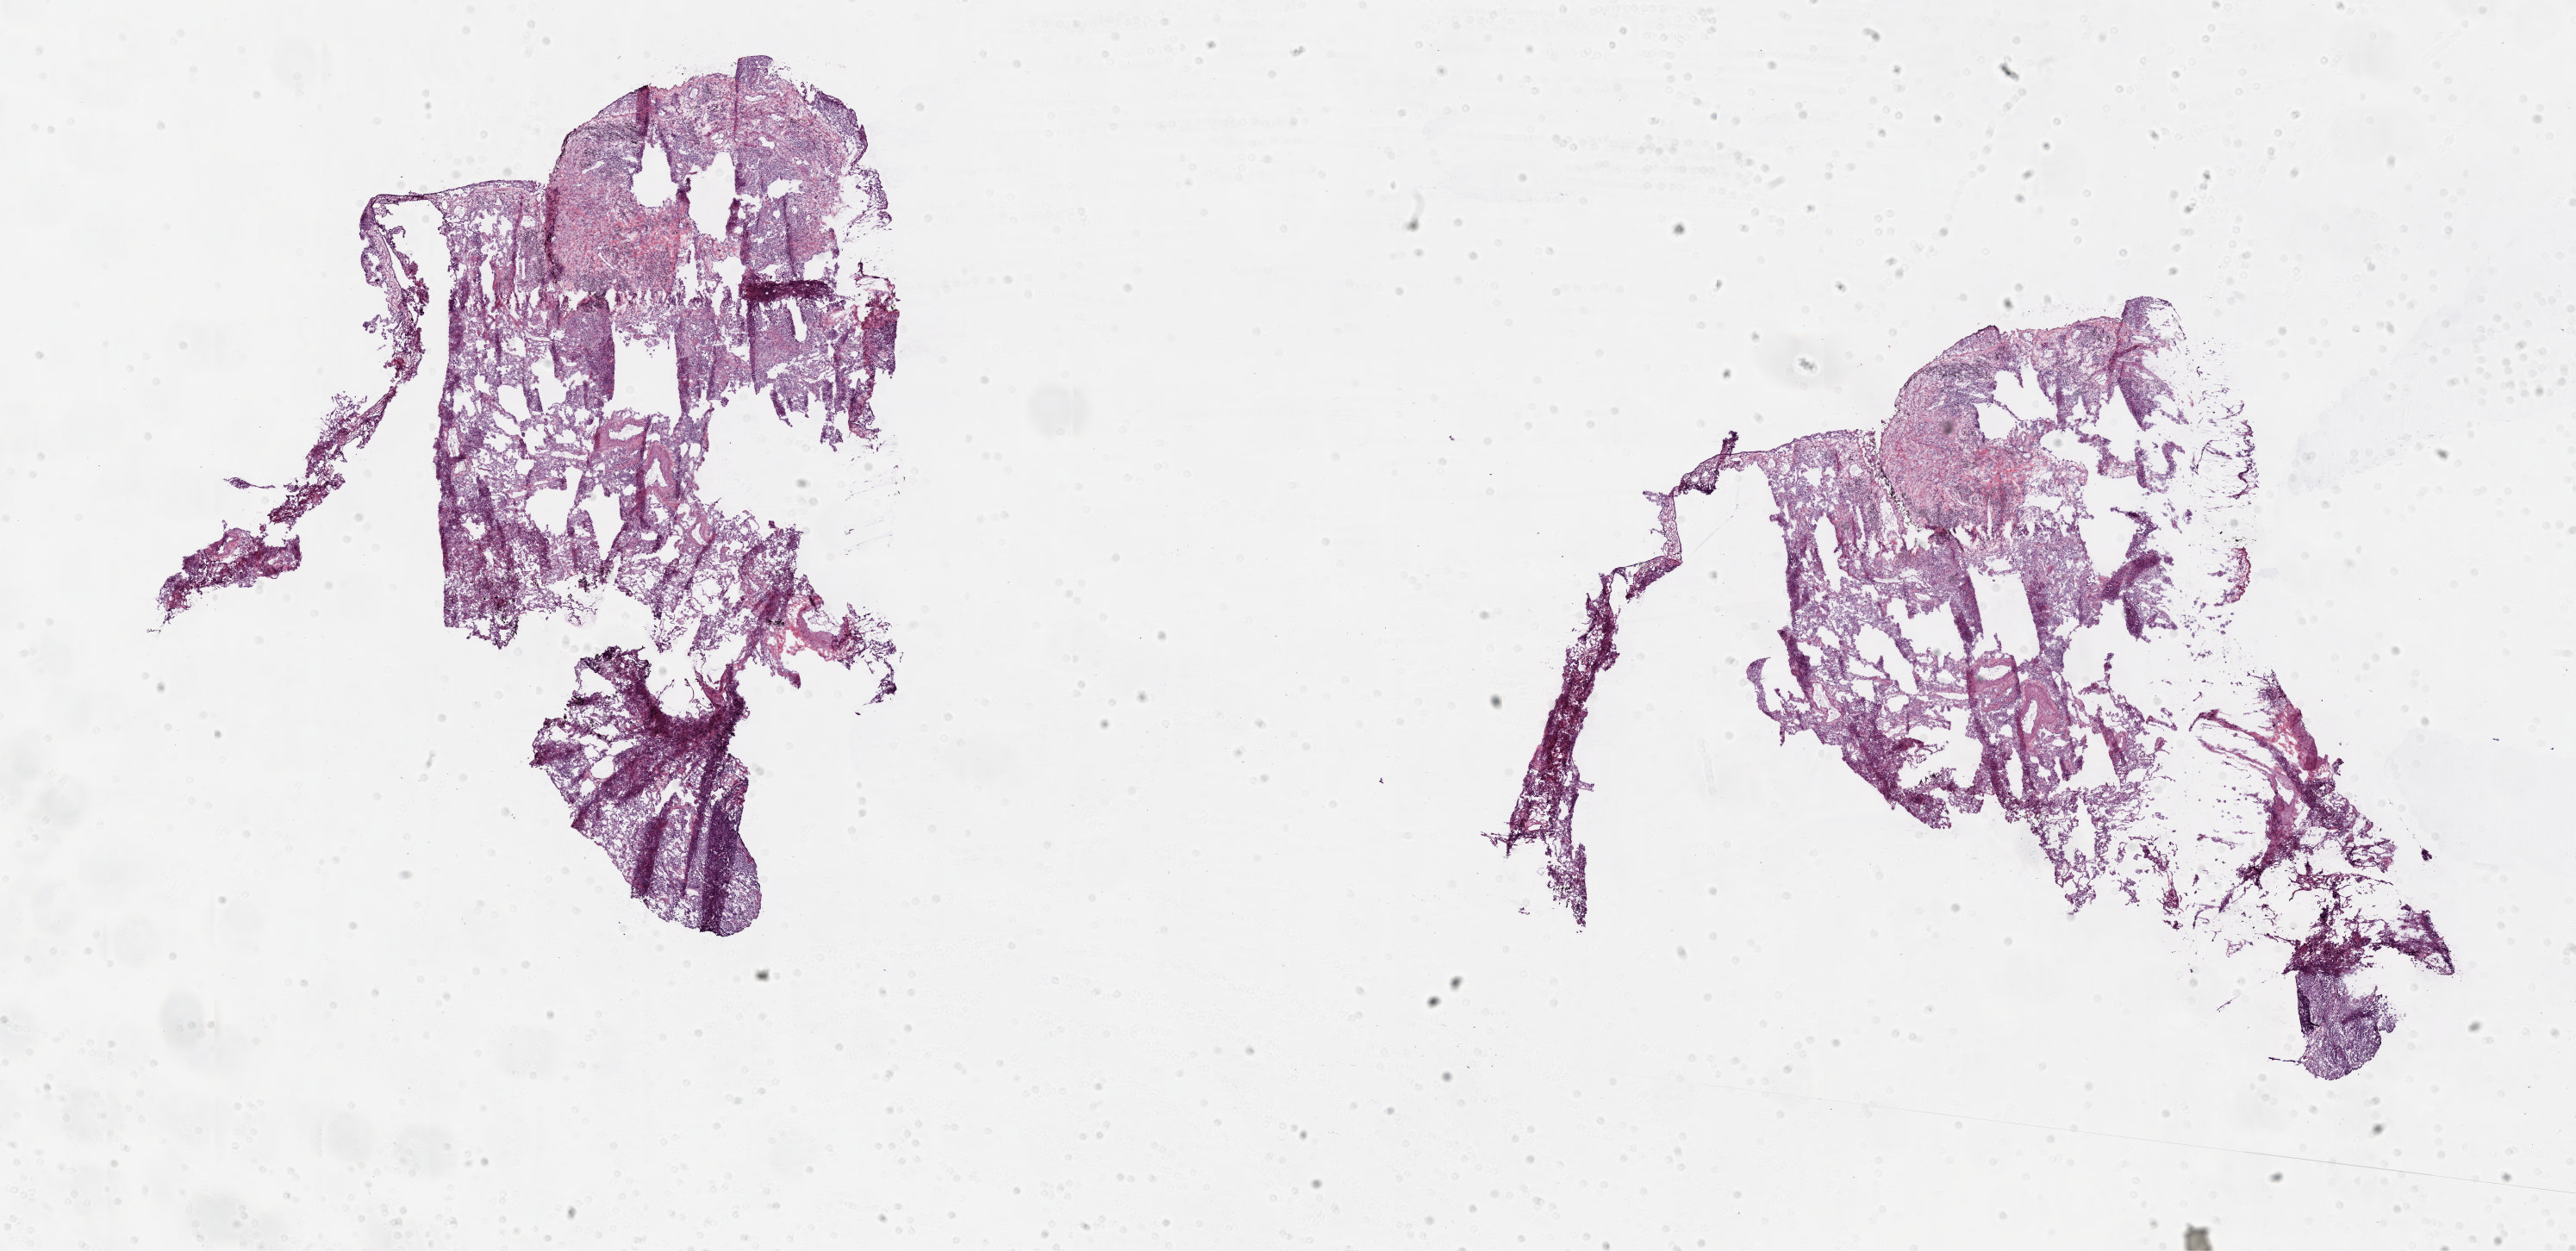
Hematoxylin and eosin (H&E) stained whole-slide image, a low-resolution overview of the entire scanned area, about 24.1 x 11.7 mm (from a 20x scan); frozen section from the top of the tissue portion; sample: solid tissue normal (non-tumour tissue), lung. Patient: male, age at initial diagnosis 64 years.
This section: solid tissue normal sample (biorepository sample class). Patient diagnosis: Adenocarcinoma, NOS (lower lobe, lung).